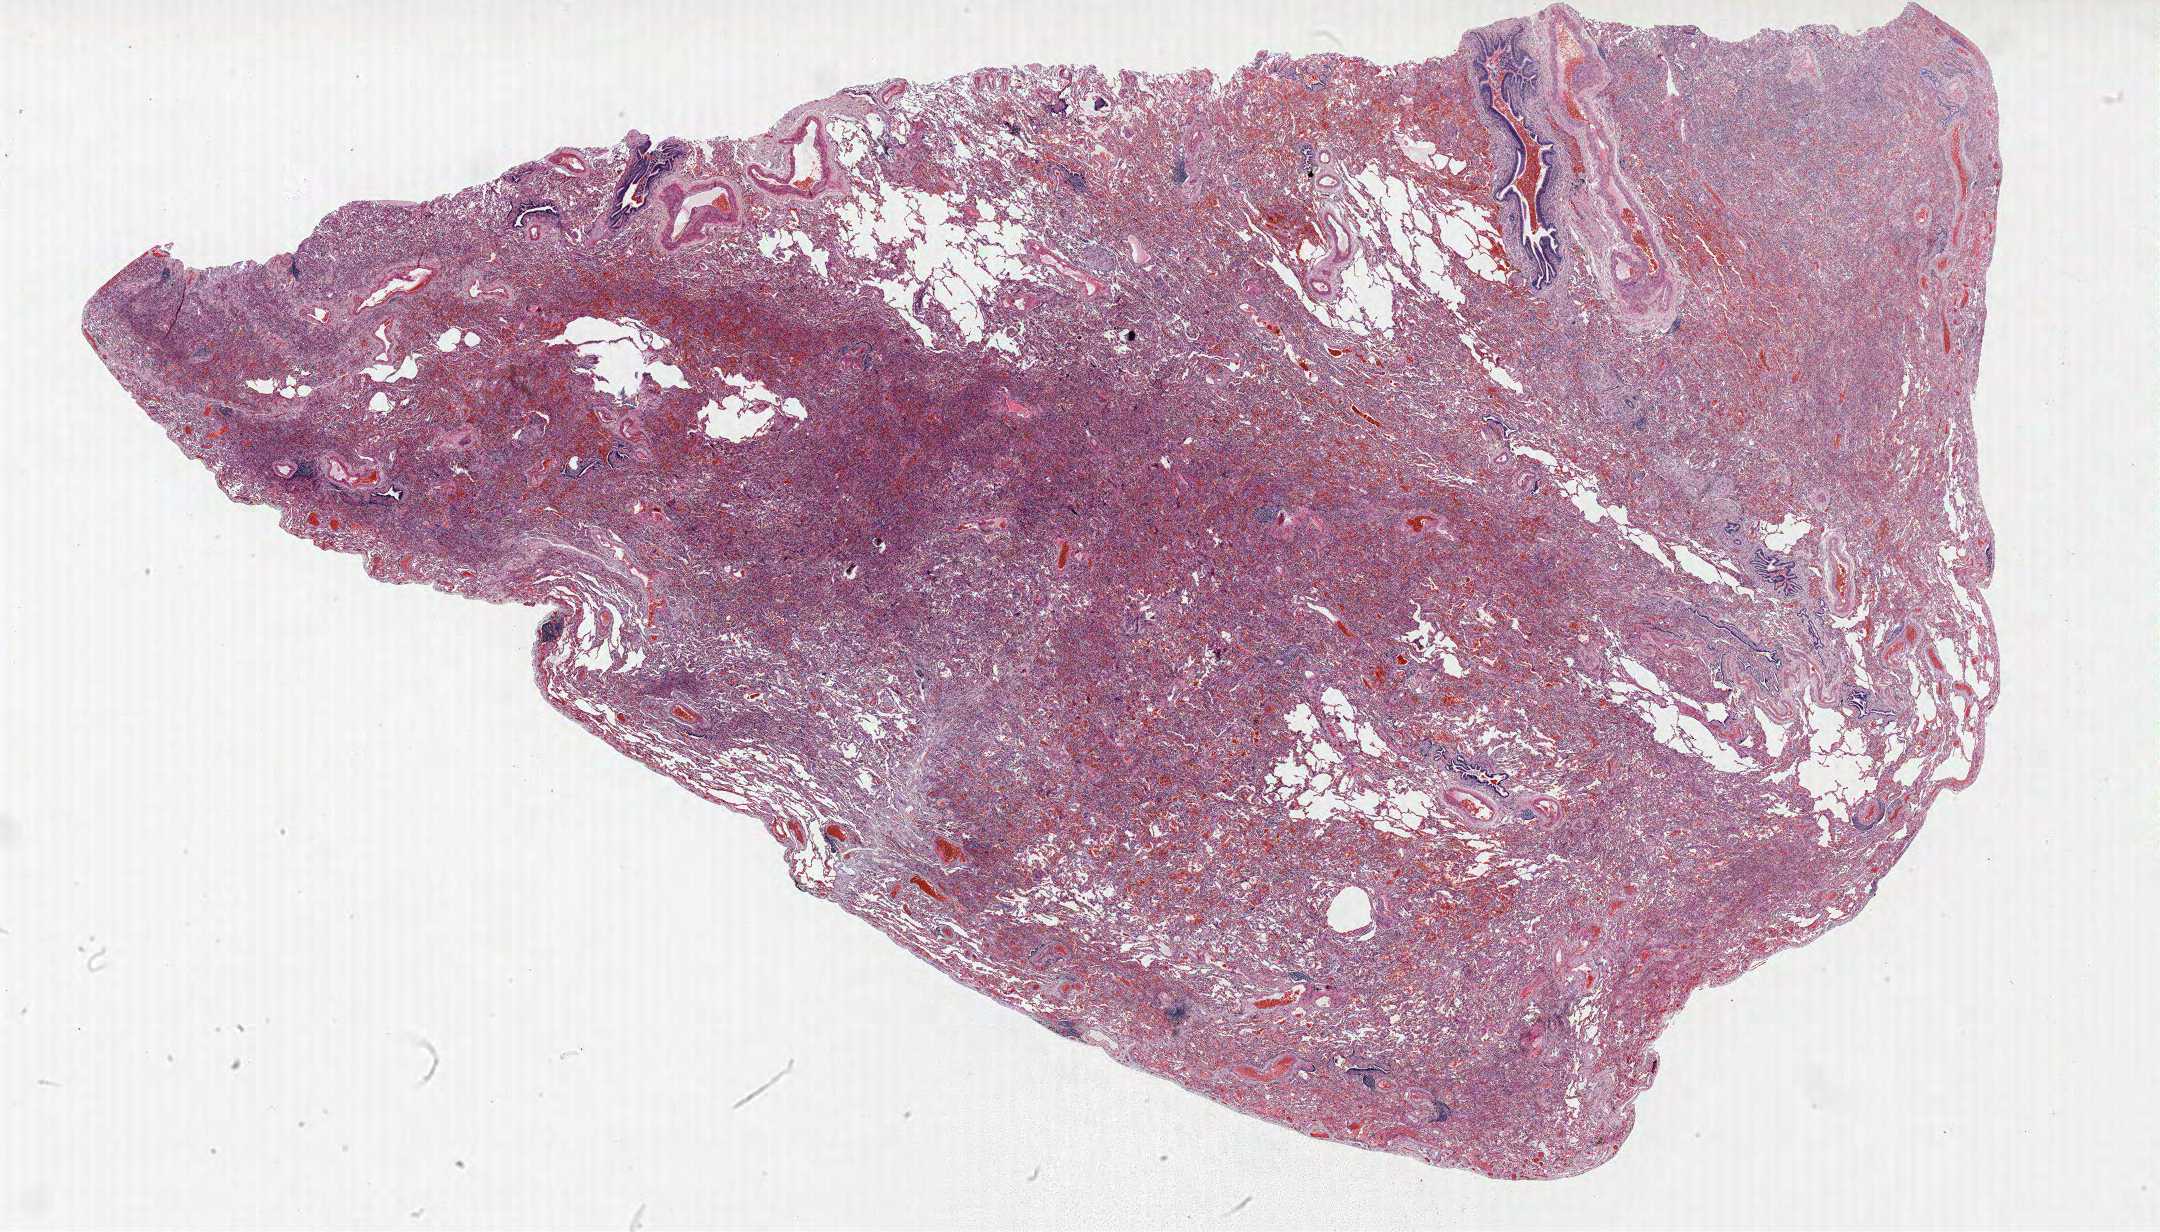
Hematoxylin and eosin (H&E) stained whole-slide image — a low-resolution overview of the entire scanned area, about 34.6 x 19.7 mm (slide scanned at 40x); formalin-fixed paraffin-embedded (FFPE) section; lung. Male patient, aged 61 at enrolment. Former smoker at enrolment.
- tumour size (pathology): 21 mm
- stage (AJCC 6th edition): IA
- primary tumour location (clinical record): right lower lobe
- ICD-O-3 topography: lower lobe of lung (C34.3)
- participant's lung-cancer diagnosis: Bronchiolo-alveolar adenocarcinoma, NOS